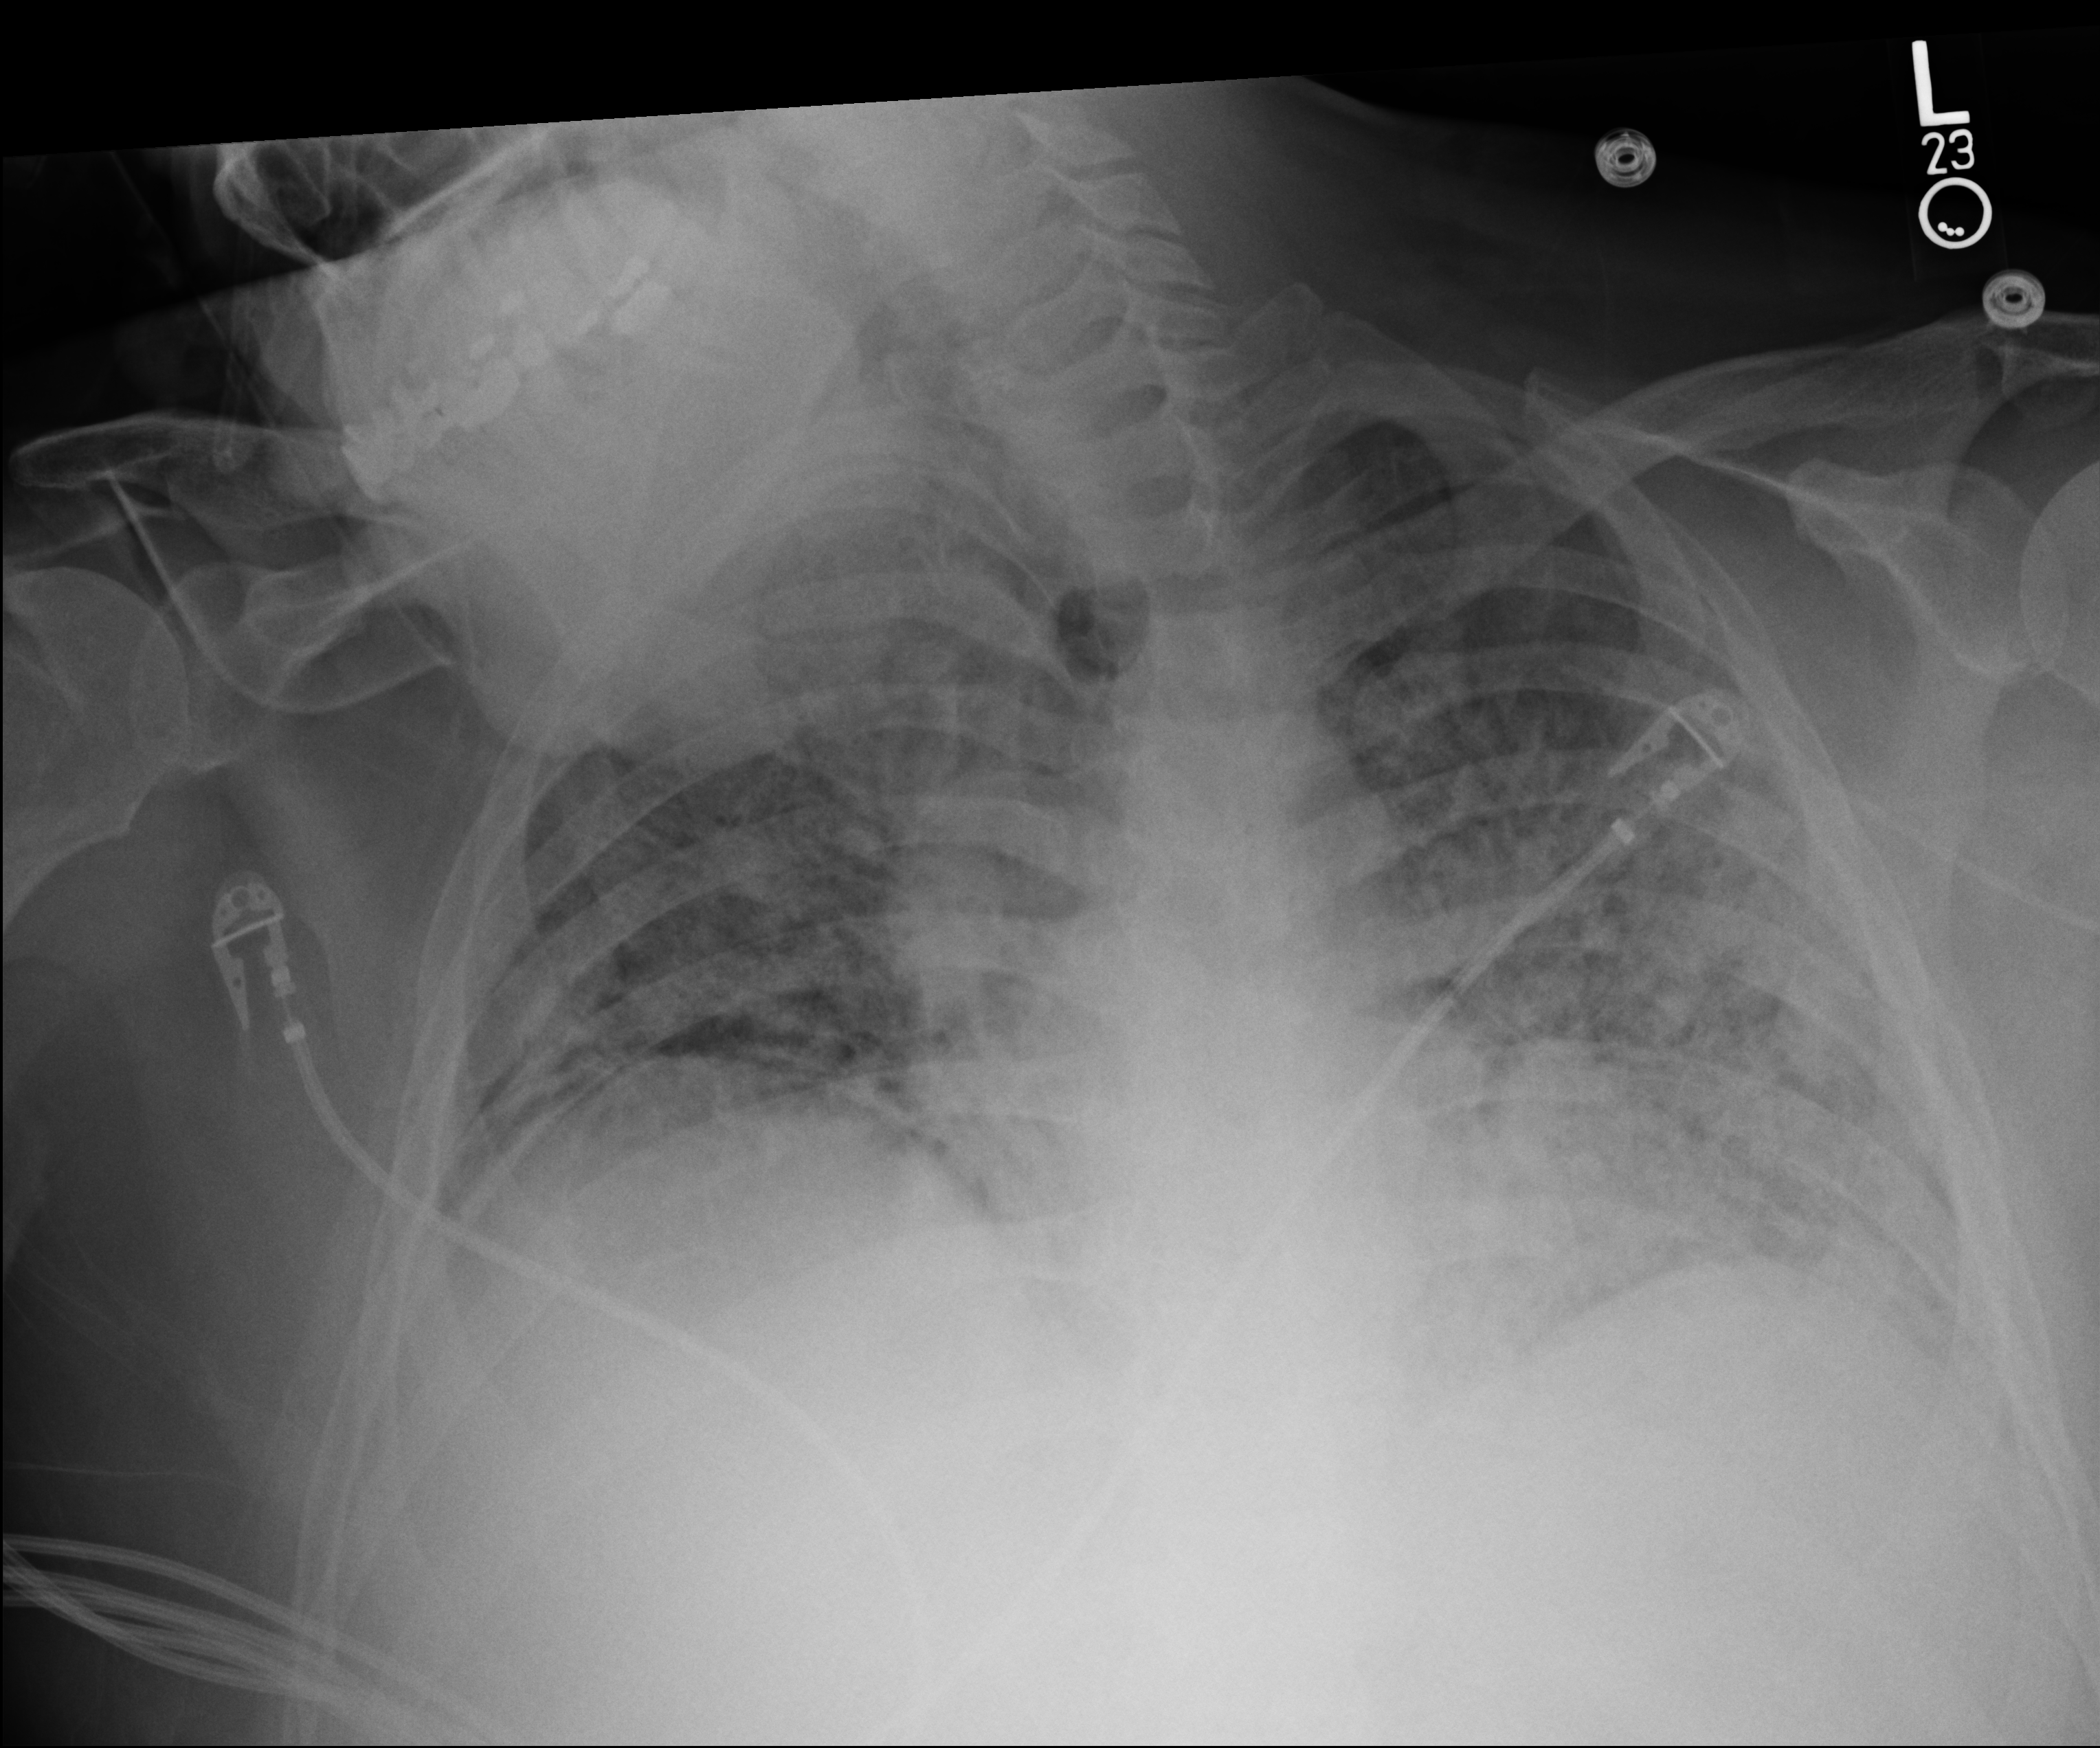
Chest X-ray (portable). Male patient hospitalised with COVID-19, age 18–59 years.
From the hospital-stay record, not from the radiograph (when in the stay this image was taken is not recorded):
- smoking status (admission record): never
- hypertension (admission record): yes
- mechanically ventilated during this hospital stay: yes